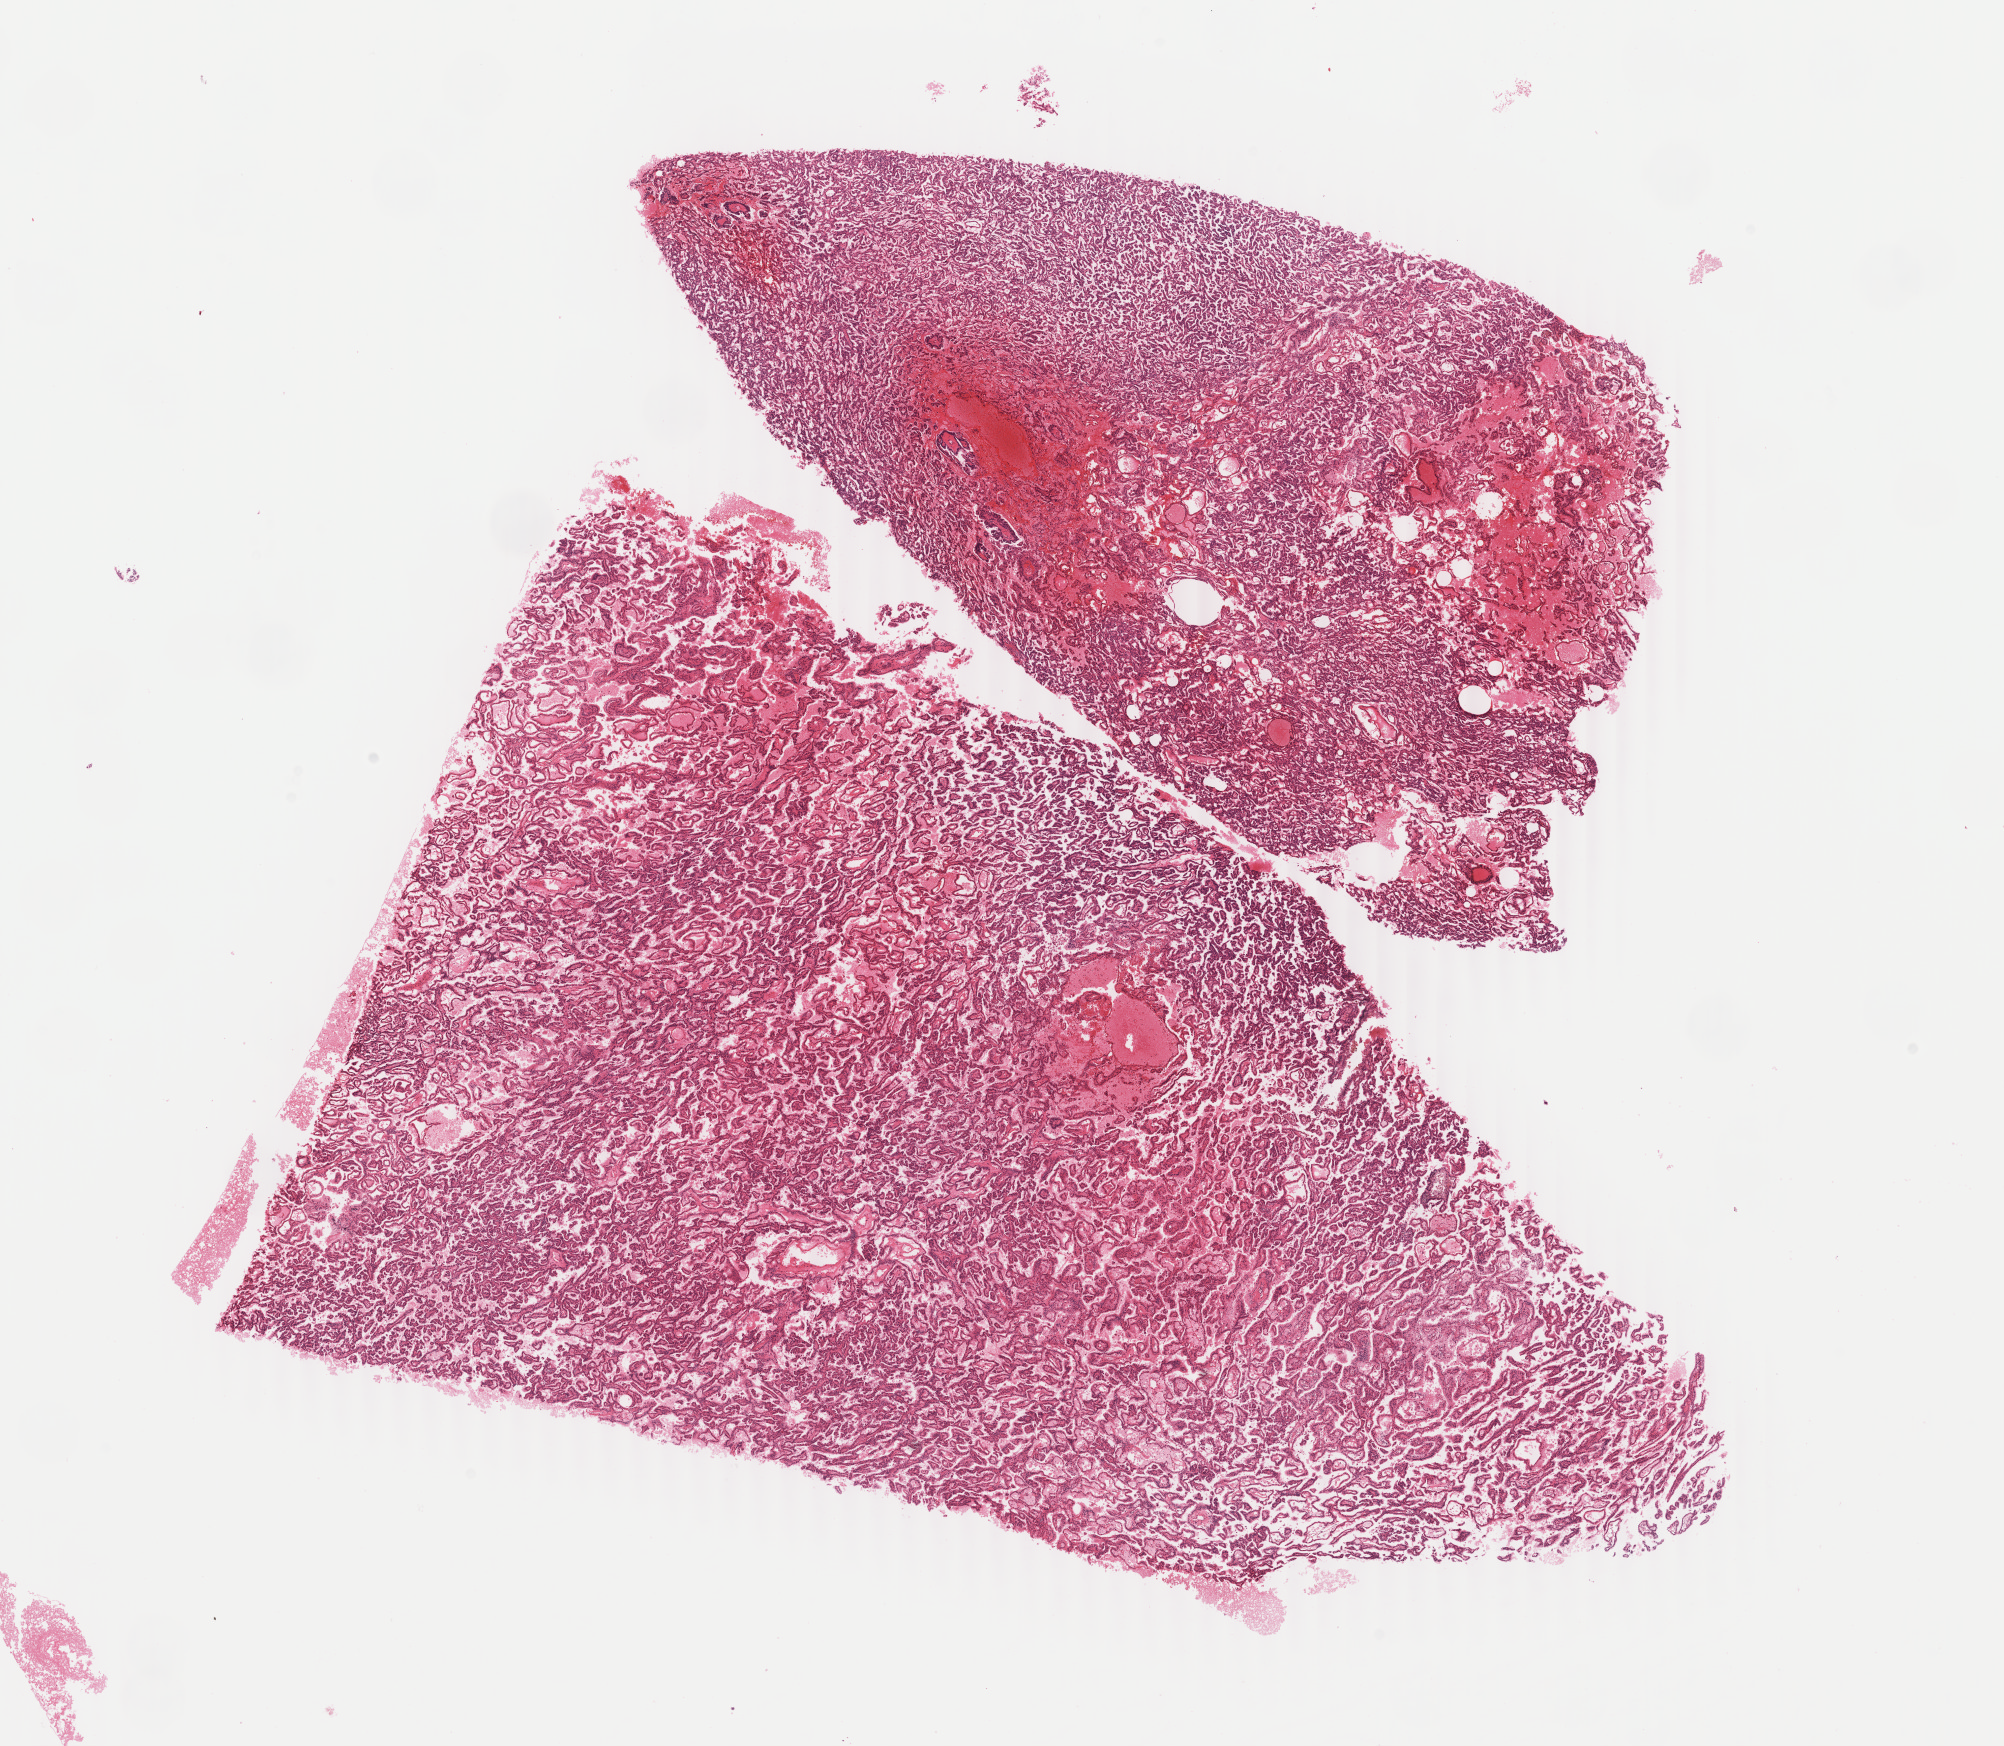
H&E whole-slide image — shown as a low-resolution overview of the whole scanned area (about 15.9 x 13.9 mm). Formalin-fixed paraffin-embedded (FFPE) diagnostic section. Primary tumour sample from the kidney. Male patient; age at initial diagnosis 74 years.
* TNM: T2 NX M0
* AJCC pathologic stage: II
* diagnosis: Papillary adenocarcinoma, NOS